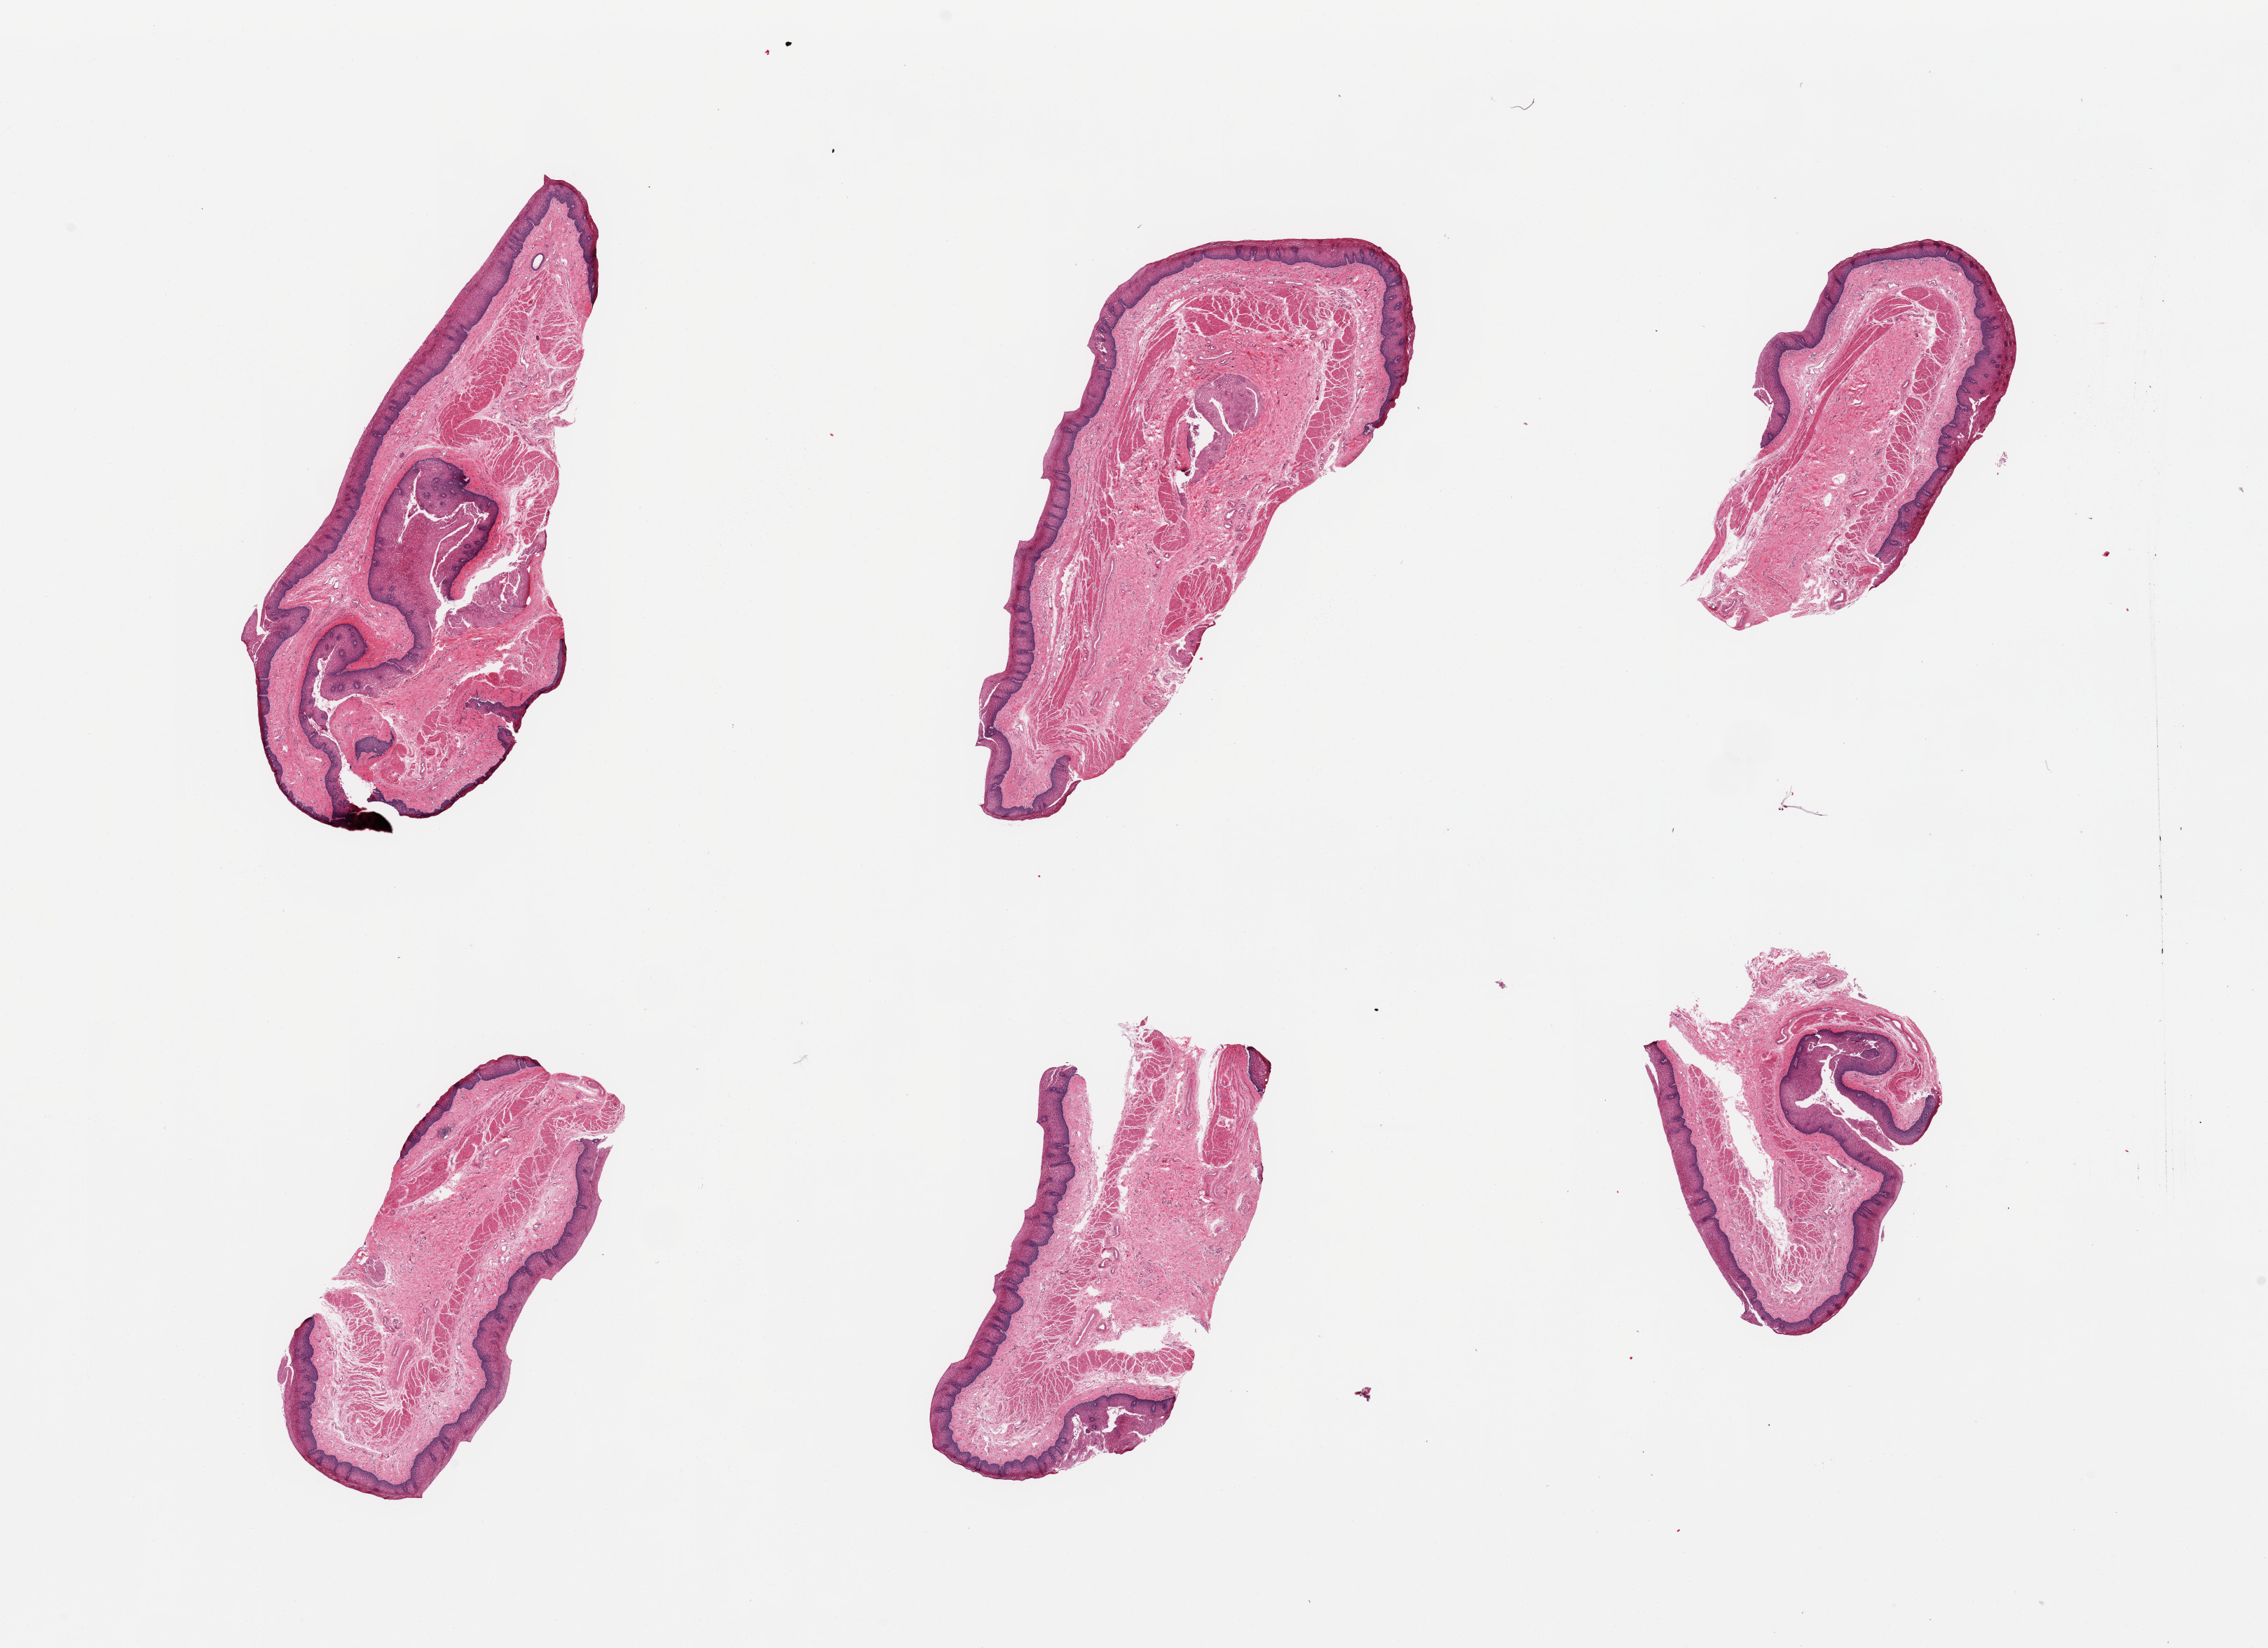
Whole-slide image, H&E stain, brightfield, a low-resolution overview of the entire scanned area, about 25.6 x 18.6 mm (acquisition: 20x scan), PAXgene-fixed paraffin-embedded (PFPE) section, sampled site (target tissue): esophageal mucous membrane, donor tissue sample. Donor sex: female.
Reviewer comment on this tissue sample: 6 pieces.